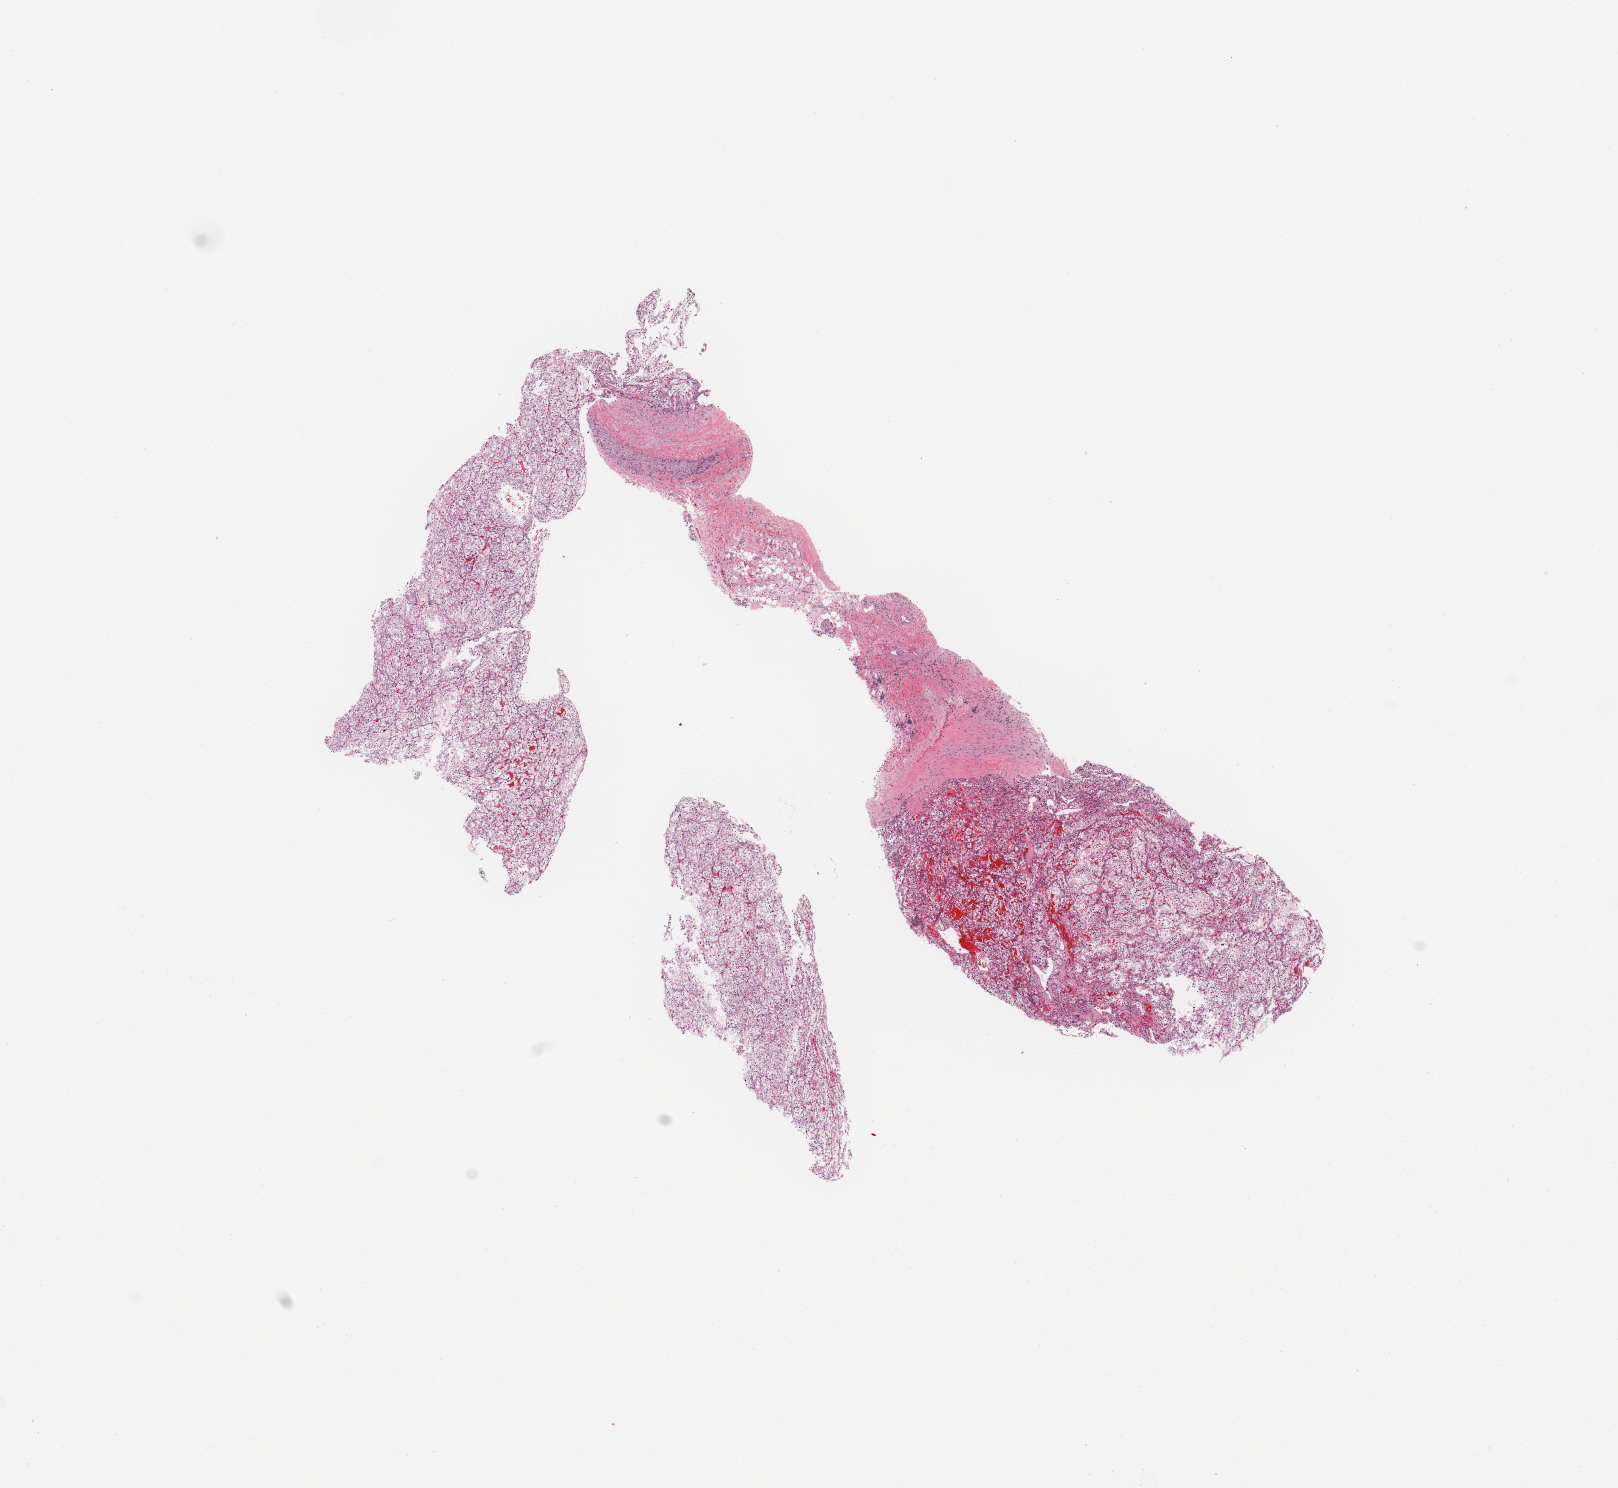
Digitized Hematoxylin and eosin (H&E) stained tissue section (whole slide) — shown as a low-resolution overview of the whole scanned area (about 12.8 x 11.8 mm, from a 20x scan), tumour tissue sample, kidney. Patient: male, age 85 years. Histologic grade: G2 (moderately differentiated).
- AJCC pathologic stage: III
- diagnosis: Renal cell carcinoma, NOS
- primary tumour site (as recorded): lower pole